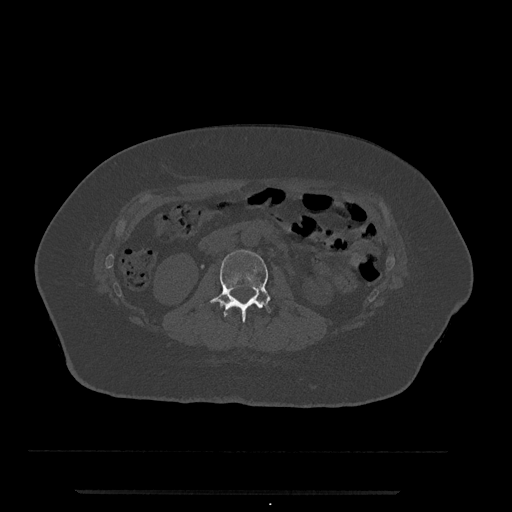
CT including the spine, one axial slice. Slice 37 of 797 in the series (ordered by position). Bone window (W 1800 / L 400 HU). 512 × 512 image matrix, field of view 440 × 440 mm. Female patient, age 51 years. From the clinical record (not read from this slice): primary cancer: neuro.
Annotated regions visible in this slice (semi-automatically segmented with operator editing):
- L2 vertebra: bounding box <200,250,271,322> (left, top, right, bottom; pixels)